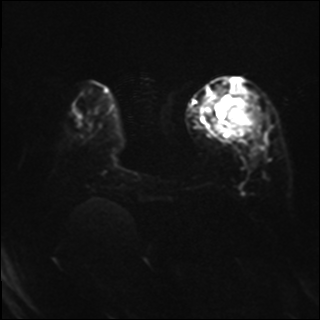
Breast MRI, one axial slice; slice 8 of 37 in the series (ordered by position); diffusion-weighted series; image 2 of 4 stored at this slice position (different b-values; order by instance number); 1.5 T; 320 × 320 image matrix. Female patient.
Structures marked on this image (expert manual segmentation):
- tumour on diffusion-weighted imaging: bounding box [x1, y1, x2, y2] px = [218, 93, 259, 138]